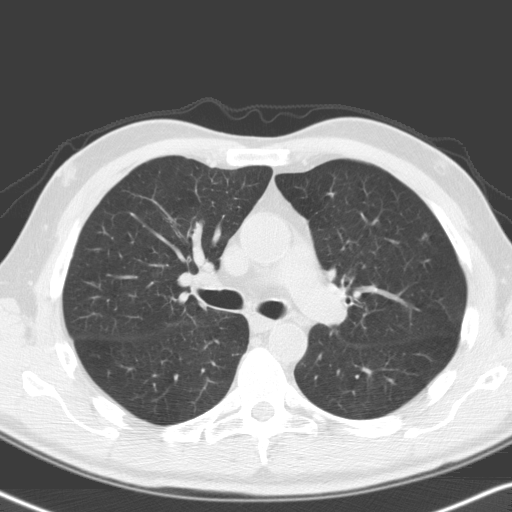
Axial slice from a low-dose chest CT screening exam; first (baseline) screen; lung window (W 1500 / L -600 HU); standard (soft-tissue) reconstruction kernel (C); 120 kVp; slice 60 of 164 in the series; 512 × 512 image matrix, field of view 329 × 329 mm. Male, age 68 years at enrolment. Former smoker at enrolment.
Expert reader's lesion annotation, box from (x=405, y=224) to (x=443, y=262) px. No non-calcified nodule or mass ≥4 mm was recorded by the screening reader at this exam. Participant outcome: lung cancer diagnosed 1047 days after this screen (after the third annual screen) — adenocarcinoma, NOS, left upper lobe, moderately differentiated (G2), stage IA (AJCC 6th edition), 6 mm at pathology.